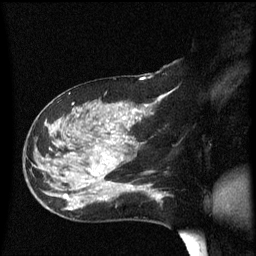
Breast MRI (dynamic contrast-enhanced), one sagittal slice. Slice 29 of 60 in the series (ordered by position). Dynamic contrast-enhanced series, image 2 of 3 at this slice position (ordered by acquisition). 1.5 T. TE 4.2 ms, TR 8.4 ms. 2.2 mm slice thickness. 256 × 256 image matrix, field of view 200 × 200 mm. Female patient, age 47 years.
Outlined on this slice (semi-automatic segmentation, software-assisted and operator-edited):
- analysis volume of interest (the breast-tissue region the enhancement analysis was run in; not a lesion): bounding box (x1, y1, x2, y2) in pixels: (24, 97, 149, 206)
- tumour enhancement mask (voxels above the 70 % enhancement threshold inside the analysis volume of interest): (64, 105, 147, 199)